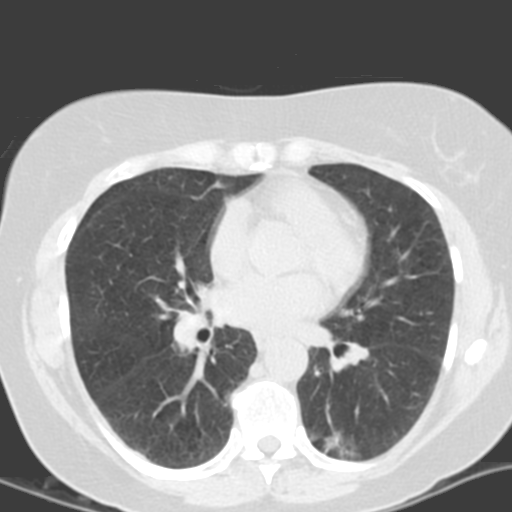
Axial slice from a low-dose chest CT screening exam; second screening round (one year after baseline); lung window (W 1500 / L -600 HU); 3.2 mm slice thickness; 120 kVp; 512 × 512 image matrix. Female, age 55 years at enrolment. Current smoker at enrolment.
• Lesion marked by an expert reader, bounding box [x1, y1, x2, y2] px = [305, 411, 378, 467].
• The screening reader recorded 4 non-calcified nodules or masses ≥4 mm on this exam (left lower lobe, left lower lobe, left upper lobe, right middle lobe); which of them this box marks is not recorded.
• Official screen result: positive, other.
• Later outcome: lung cancer diagnosed 688 days after this screen — adenocarcinoma with mixed subtypes, left lower lobe, poorly differentiated (G3), stage IA (AJCC 6th edition), 21 mm at pathology.